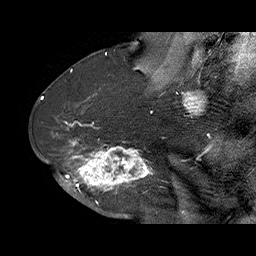
Breast MRI (dynamic contrast-enhanced), one sagittal slice; position 38 of 70 along the scan axis; dynamic contrast-enhanced series, time point 2 of 6 at this slice position (early post-contrast); 1.5 T; TE 4.5 ms, TR 32.4 ms; 256 × 256 image matrix, field of view 180 × 180 mm. Female patient. Case-level facts recorded for this patient, not image findings: setting: breast cancer imaged before/during neoadjuvant chemotherapy; receptor status: HR-positive, HER2-negative.
Annotated regions visible in this slice (semi-automatic segmentation, software-assisted and operator-edited):
- analysis volume of interest (the breast-tissue region the enhancement analysis was run in; not a lesion): box from (x=71, y=128) to (x=159, y=202) px
- tumour enhancement mask (voxels above the 100 % enhancement threshold inside the analysis volume of interest): (x=71, y=138)–(x=154, y=202)